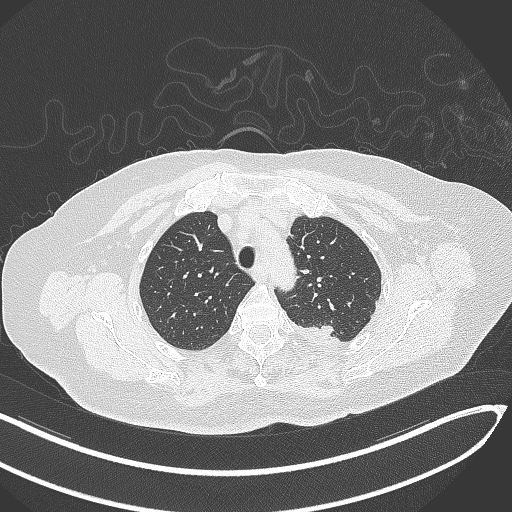
Chest CT, one axial slice. Slice 256 of 270 in the series (ordered by position). Reconstruction kernel B70f. Lung window (W 1500 / L -600 HU). 512 × 512 image matrix. Patient: female, 76 years. Case-level facts recorded for this patient, not image findings: clinical TNM (as recorded): T1c N0 M0.
Outlined on this slice (bounding box drawn by a radiologist):
- lung tumour (recorded histology: adenocarcinoma): bounding box [x1, y1, x2, y2] px = [319, 321, 332, 338]